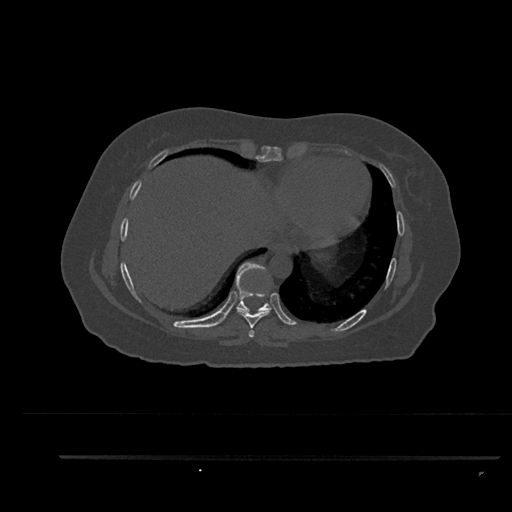
CT including the spine, one axial slice; reconstruction kernel Br40s/3; 120 kVp; bone window (W 1800 / L 400 HU); 0.5 mm slice thickness; 512 × 512 image matrix, field of view 408 × 408 mm. Patient: female, 44 years. From the clinical record (not read from this slice): primary cancer: renal; vertebrae with lytic lesions (as recorded): L1.
Structures marked on this image (semi-automatically segmented with operator editing):
- T7 vertebra: bounding box [x1, y1, x2, y2] px = [248, 329, 255, 338]
- T8 vertebra: [237, 310, 271, 329]
- T9 vertebra: [235, 262, 272, 312]